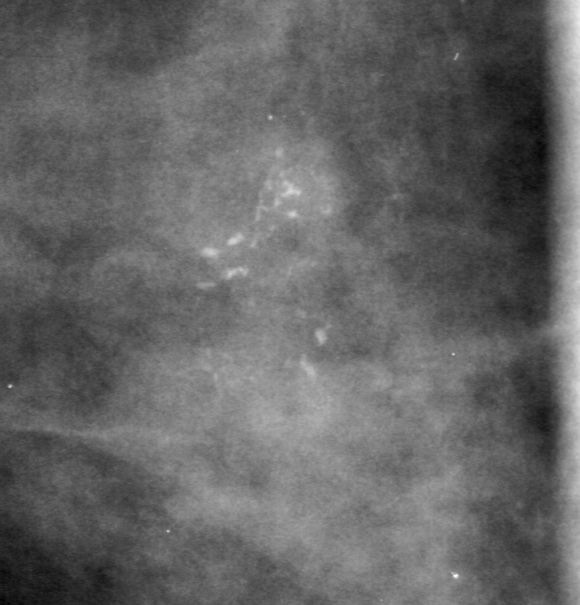
Region of interest cut from a scanned film mammogram (one marked finding), right breast, CC view, BI-RADS breast density category 3 (scale 1–4).
Finding: calcifications, morphology fine linear branching, distribution clustered; BI-RADS assessment category 3; subtlety rating 5 on a 1 (subtle) to 5 (obvious) scale; pathology (as recorded): malignant.